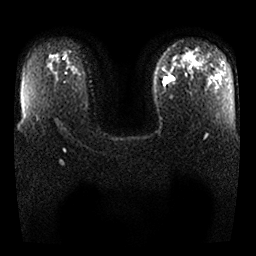
Breast MRI, one axial slice; position 15 of 25 along the scan axis; diffusion-weighted series; image 2 of 4 stored at this slice position (different b-values; order by instance number); 1.5 T; 256 × 256 image matrix, field of view 340 × 340 mm. Female patient.
Outlined on this slice (expert manual segmentation):
- tumour on diffusion-weighted imaging: box from (x=162, y=75) to (x=173, y=86) px